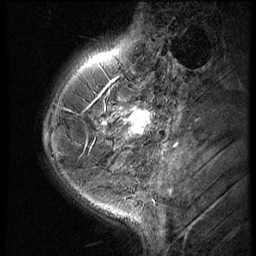
Breast MRI (dynamic contrast-enhanced), one sagittal slice; slice 18 of 60 in the series (ordered by position); 3 images stored at this slice position (order not interpretable as contrast timing); 1.5 T; TE 4.2 ms, TR 9 ms; 2.5 mm slice thickness; 256 × 256 image matrix, field of view 180 × 180 mm. Patient: female, 38 years. From the clinical record (not read from this slice): setting: breast cancer imaged before/during neoadjuvant chemotherapy; receptor status: triple-negative.
Structures marked on this image (semi-automatically segmented with operator editing):
- analysis volume of interest (the breast-tissue region the enhancement analysis was run in; not a lesion): bounding box [x1, y1, x2, y2] px = [119, 93, 165, 150]
- tumour enhancement mask (voxels above the 140 % enhancement threshold inside the analysis volume of interest): [119, 108, 155, 140]